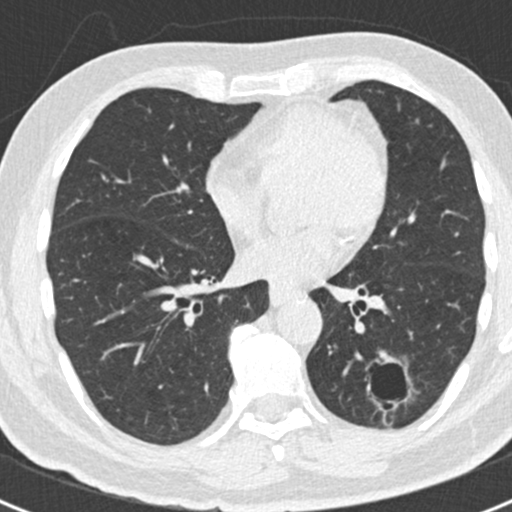
Low-dose screening chest CT, axial slice; baseline screening round; lung window (W 1500 / L -600 HU); 512 × 512 image matrix, field of view 300 × 300 mm. Male, age 66 years at enrolment. Former smoker at enrolment.
Expert reader's lesion annotation, box from (x=345, y=341) to (x=421, y=420) px. Reader record for this screening exam (exam-level; its link to the box is not recorded): non-calcified nodule or mass ≥4 mm, left lower lobe, 43 × 27 mm, smooth margins. Lung cancer was diagnosed 801 days after this screen (after the third annual screen): adenocarcinoma, NOS, left lower lobe, poorly differentiated (G3), stage IB (AJCC 6th edition), 38 mm at pathology.